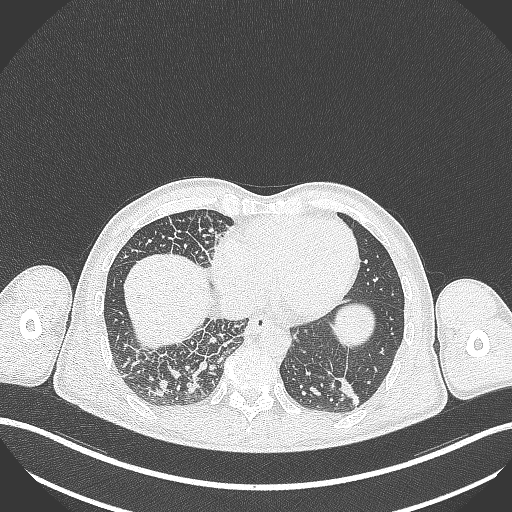
Chest CT, one axial slice; slice 85 of 348 in the series (ordered by position); 120 kVp; lung window (W 1500 / L -600 HU); 1 mm slice thickness; 512 × 512 image matrix, field of view 400 × 400 mm. Male patient, age 49 years. From the clinical record (not read from this slice): clinical TNM (as recorded): T2b N1 M0.
Annotated regions visible in this slice (rectangle marked by the reading radiologist):
- lung tumour (recorded histology: adenocarcinoma): bounding box [x1, y1, x2, y2] px = [335, 377, 363, 408]